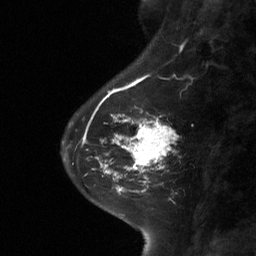
Breast MRI (dynamic contrast-enhanced), one sagittal slice; slice 21 of 64 in the series (ordered by position); dynamic contrast-enhanced study with each time point stored as its own series, time point 2 of 3 at this slice position (early post-contrast, ordered by acquisition time); 1.5 T; TE 4.8 ms, TR 27 ms; 2 mm slice thickness; 256 × 256 image matrix, field of view 180 × 180 mm. Female patient, age 42 years. From the clinical record (not read from this slice): setting: breast cancer imaged before/during neoadjuvant chemotherapy; receptor status: triple-negative.
Structures marked on this image (semi-automatically segmented with operator editing):
- analysis volume of interest (the breast-tissue region the enhancement analysis was run in; not a lesion): bounding box <111,104,179,178> (left, top, right, bottom; pixels)
- tumour enhancement mask (voxels above the 90 % enhancement threshold inside the analysis volume of interest): <111,114,176,178>